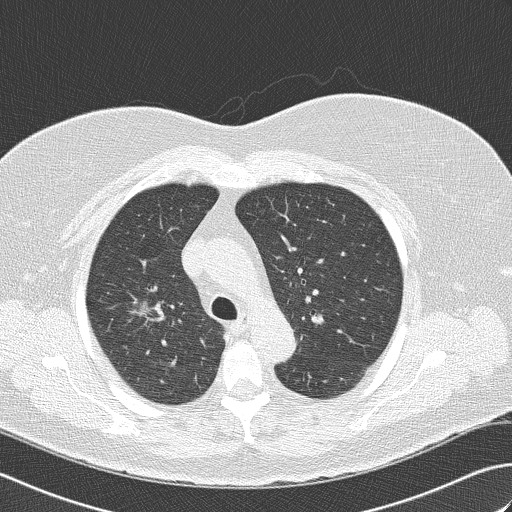
Low-dose screening chest CT, axial slice. Second annual screen. Lung window (W 1500 / L -600 HU). 2 mm slice thickness. Lung (sharp) reconstruction kernel (B50f). Female participant, aged 74 years at enrolment. Former smoker at enrolment.
Expert reader's lesion annotation, bounding box [x1, y1, x2, y2] px = [103, 281, 176, 340]. The screening reader recorded 4 non-calcified nodules or masses ≥4 mm on this exam (right upper lobe, right middle lobe, right middle lobe, left lower lobe); which of them this box marks is not recorded. Official screen result: positive, other. Later outcome: lung cancer diagnosed 453 days after this screen (after the third annual screen) — bronchiolo-alveolar carcinoma, non-mucinous, right upper lobe, well differentiated (G1), stage IA (AJCC 6th edition), 14 mm at pathology.